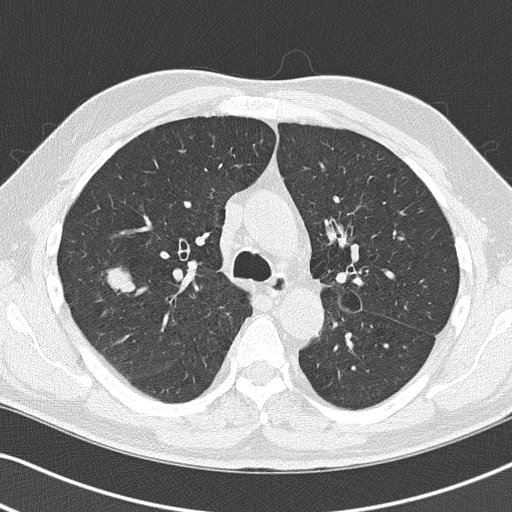
Low-dose screening chest CT, one axial slice; slice 88 of 140 in the series (ordered by position); lung window (W 1500 / L -600 HU); 2 mm slice thickness; 512 × 512 image matrix, field of view 330 × 330 mm.
Outlined on this slice (outlined manually by an expert reader):
- lesion 1 (tumor, upper lobe of right lung): box from (x=107, y=267) to (x=134, y=292) px